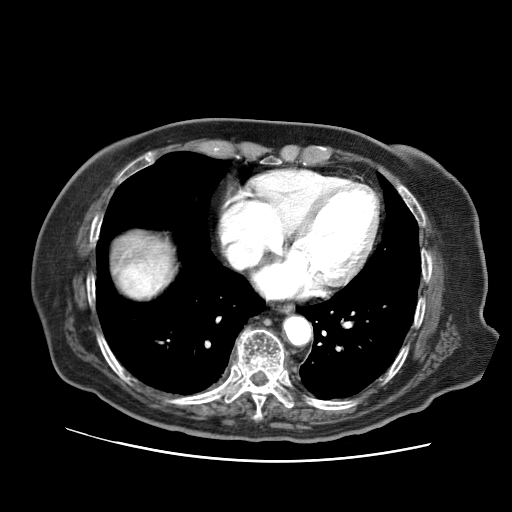
Contrast-enhanced abdominal CT (liver protocol), one axial slice. Reconstruction kernel STANDARD. 120 kVp. Soft-tissue window (W 400 / L 40 HU). 2.5 mm slice thickness. 512 × 512 image matrix, field of view 380 × 380 mm. From the clinical record (not read from this slice): diagnosis: hepatocellular carcinoma (patient treated with transarterial chemoembolisation; whether this scan precedes or follows treatment is not stated here); TNM stage (as recorded): Stage-I; Child-Pugh class: A; tumour differentiation: well differentiated; tumour nodularity: uninodular.
Outlined on this slice (semi-automatically segmented with operator editing):
- abdominal aorta: box from (x=284, y=316) to (x=310, y=344) px
- liver parenchyma outside the tumour (the mass and vessels are separate outlines, so this box may not span the whole liver): (x=114, y=234)–(x=170, y=286)
- mass: (x=117, y=263)–(x=162, y=297)